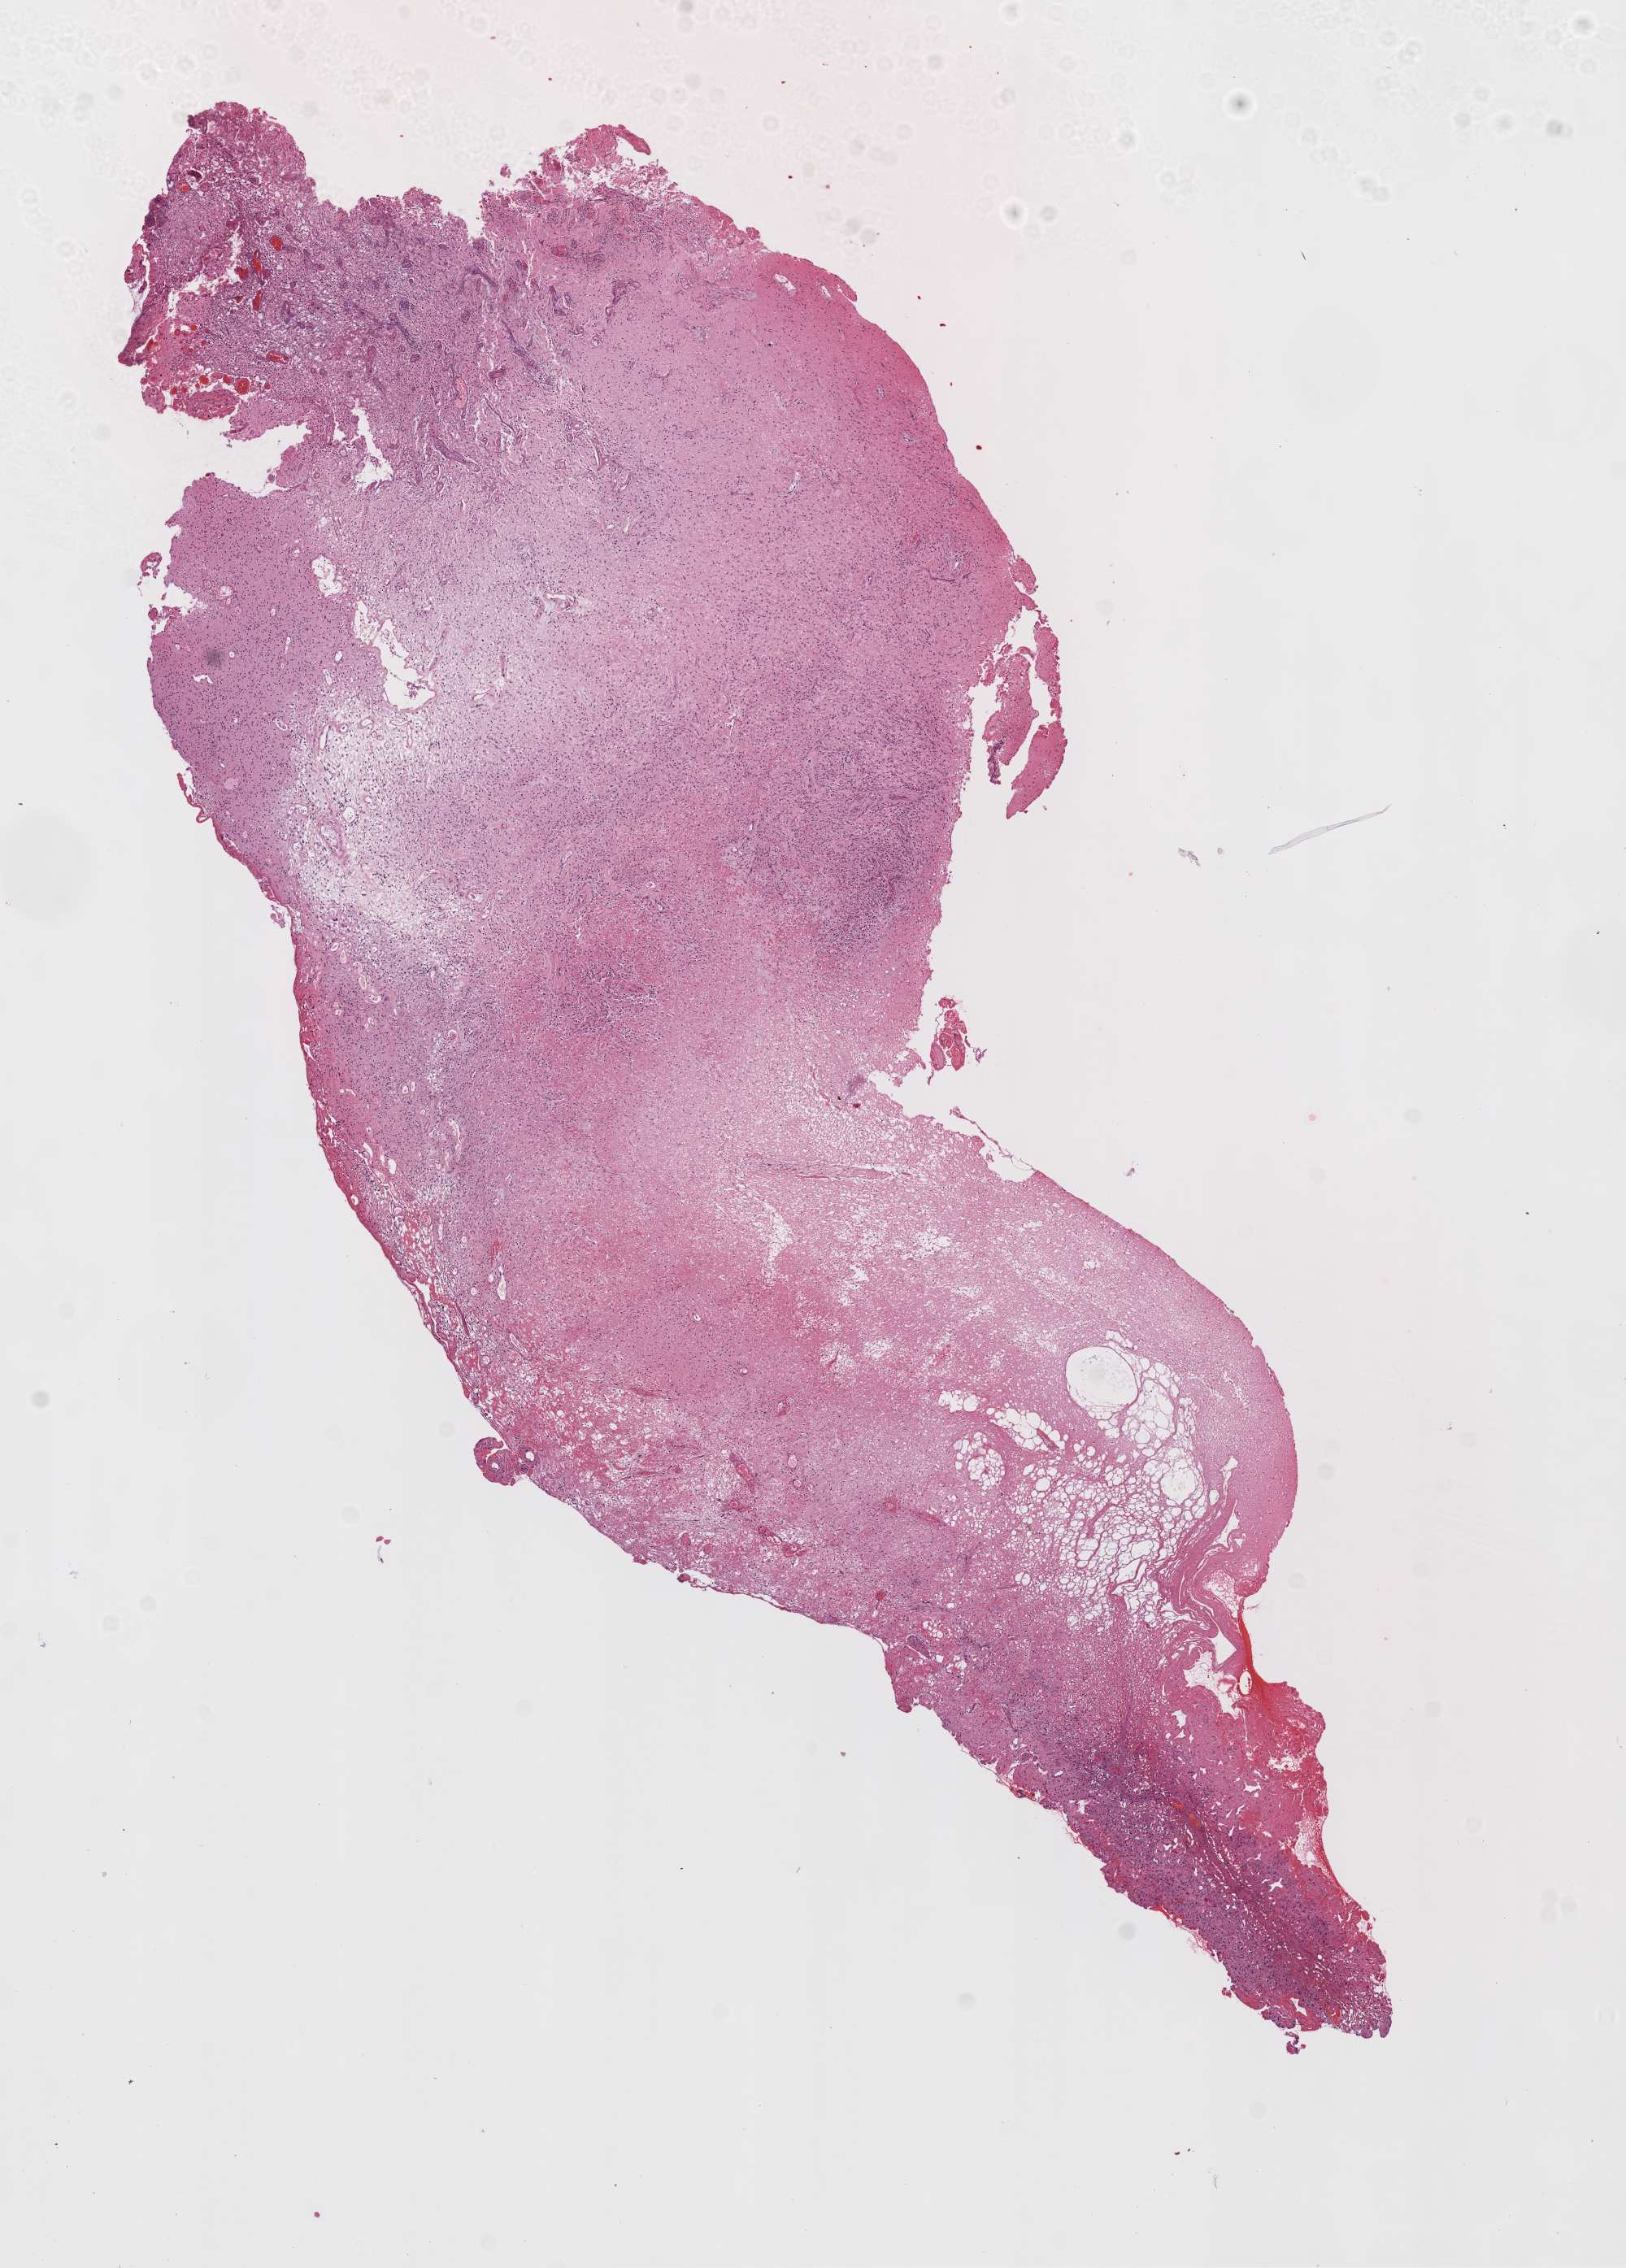
Hematoxylin and eosin (H&E) stained whole-slide image — a low-resolution overview of the entire scanned area, about 8.0 x 11.2 mm (acquisition: 20x scan). Formalin-fixed paraffin-embedded (FFPE) diagnostic section. Primary tumour sample from the brain. Female patient; age at initial diagnosis 75 years.
Histologic diagnosis: Glioblastoma.